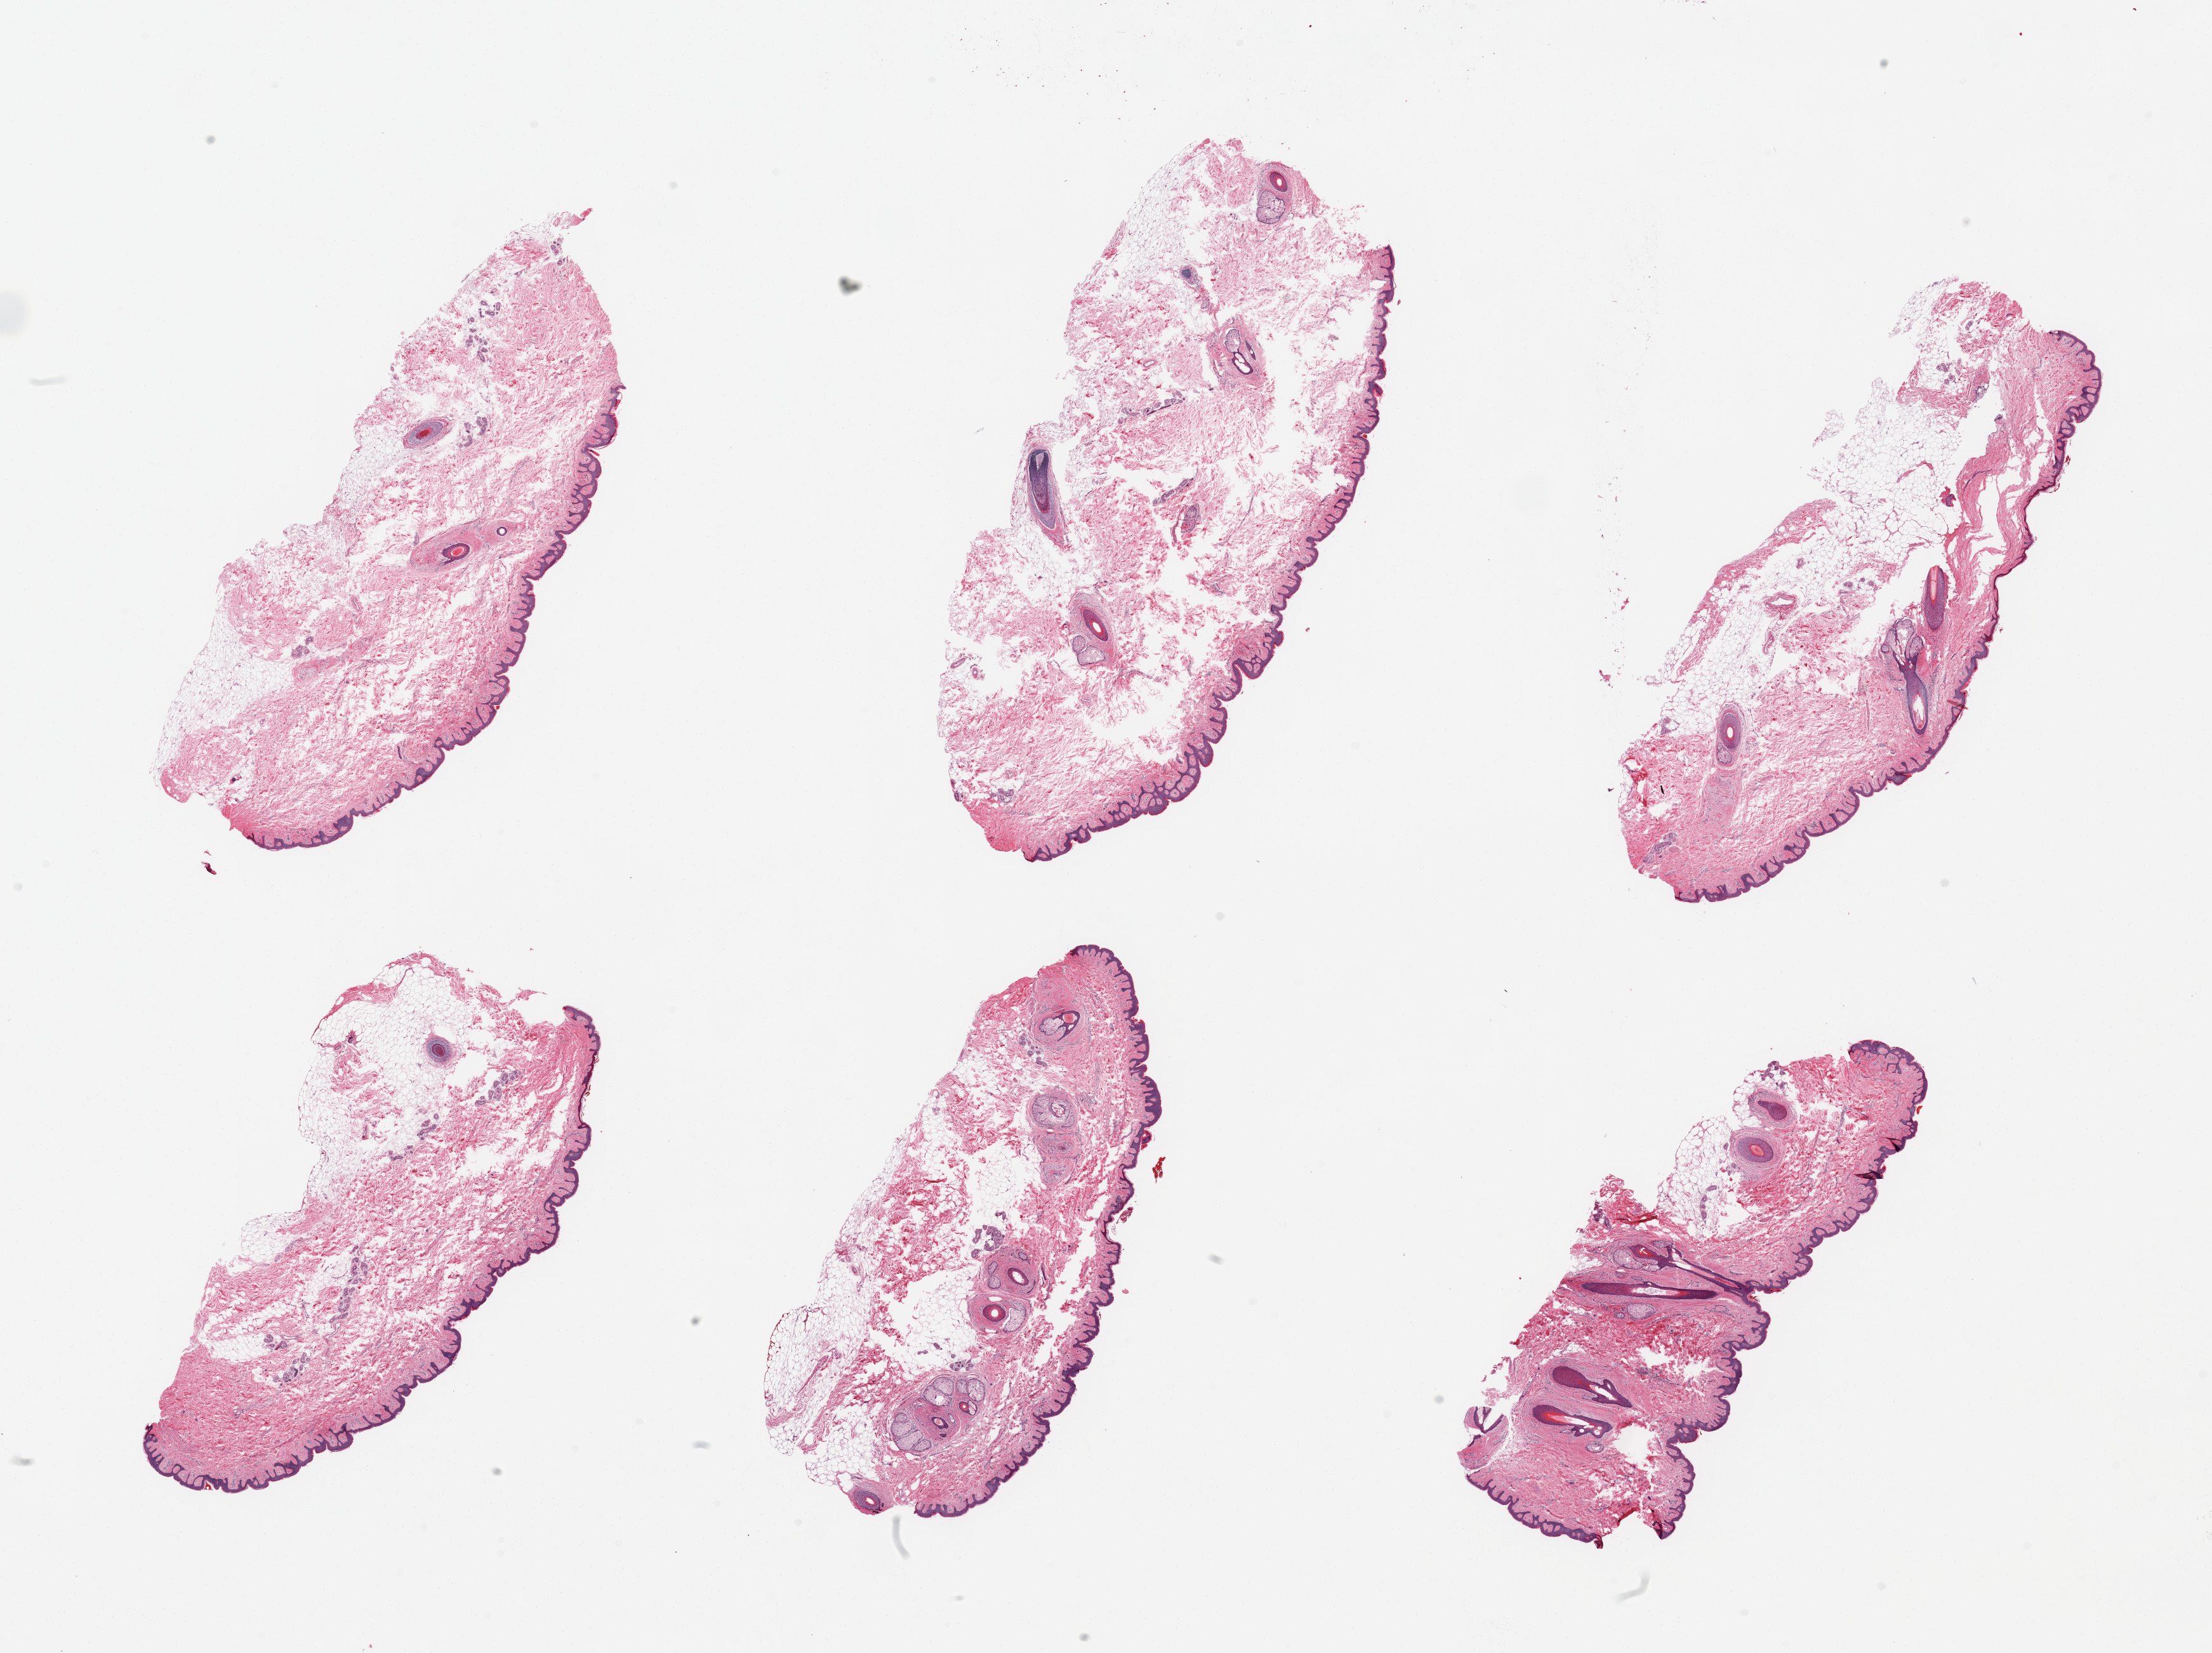
Digitized haematoxylin and eosin-stained section, low-resolution overview of the scanned area, about 27.6 x 20.6 mm (slide scanned at 20x); PAXgene-fixed paraffin-embedded (PFPE) section; sampled site (target tissue): skin of suprapubic region; donor tissue sample. Donor sex: male.
Pathologist's review note for this sample: 6 pieces; hair-bearing skin with up to 6 hair follicles per piece; up to 40% dermal fat.